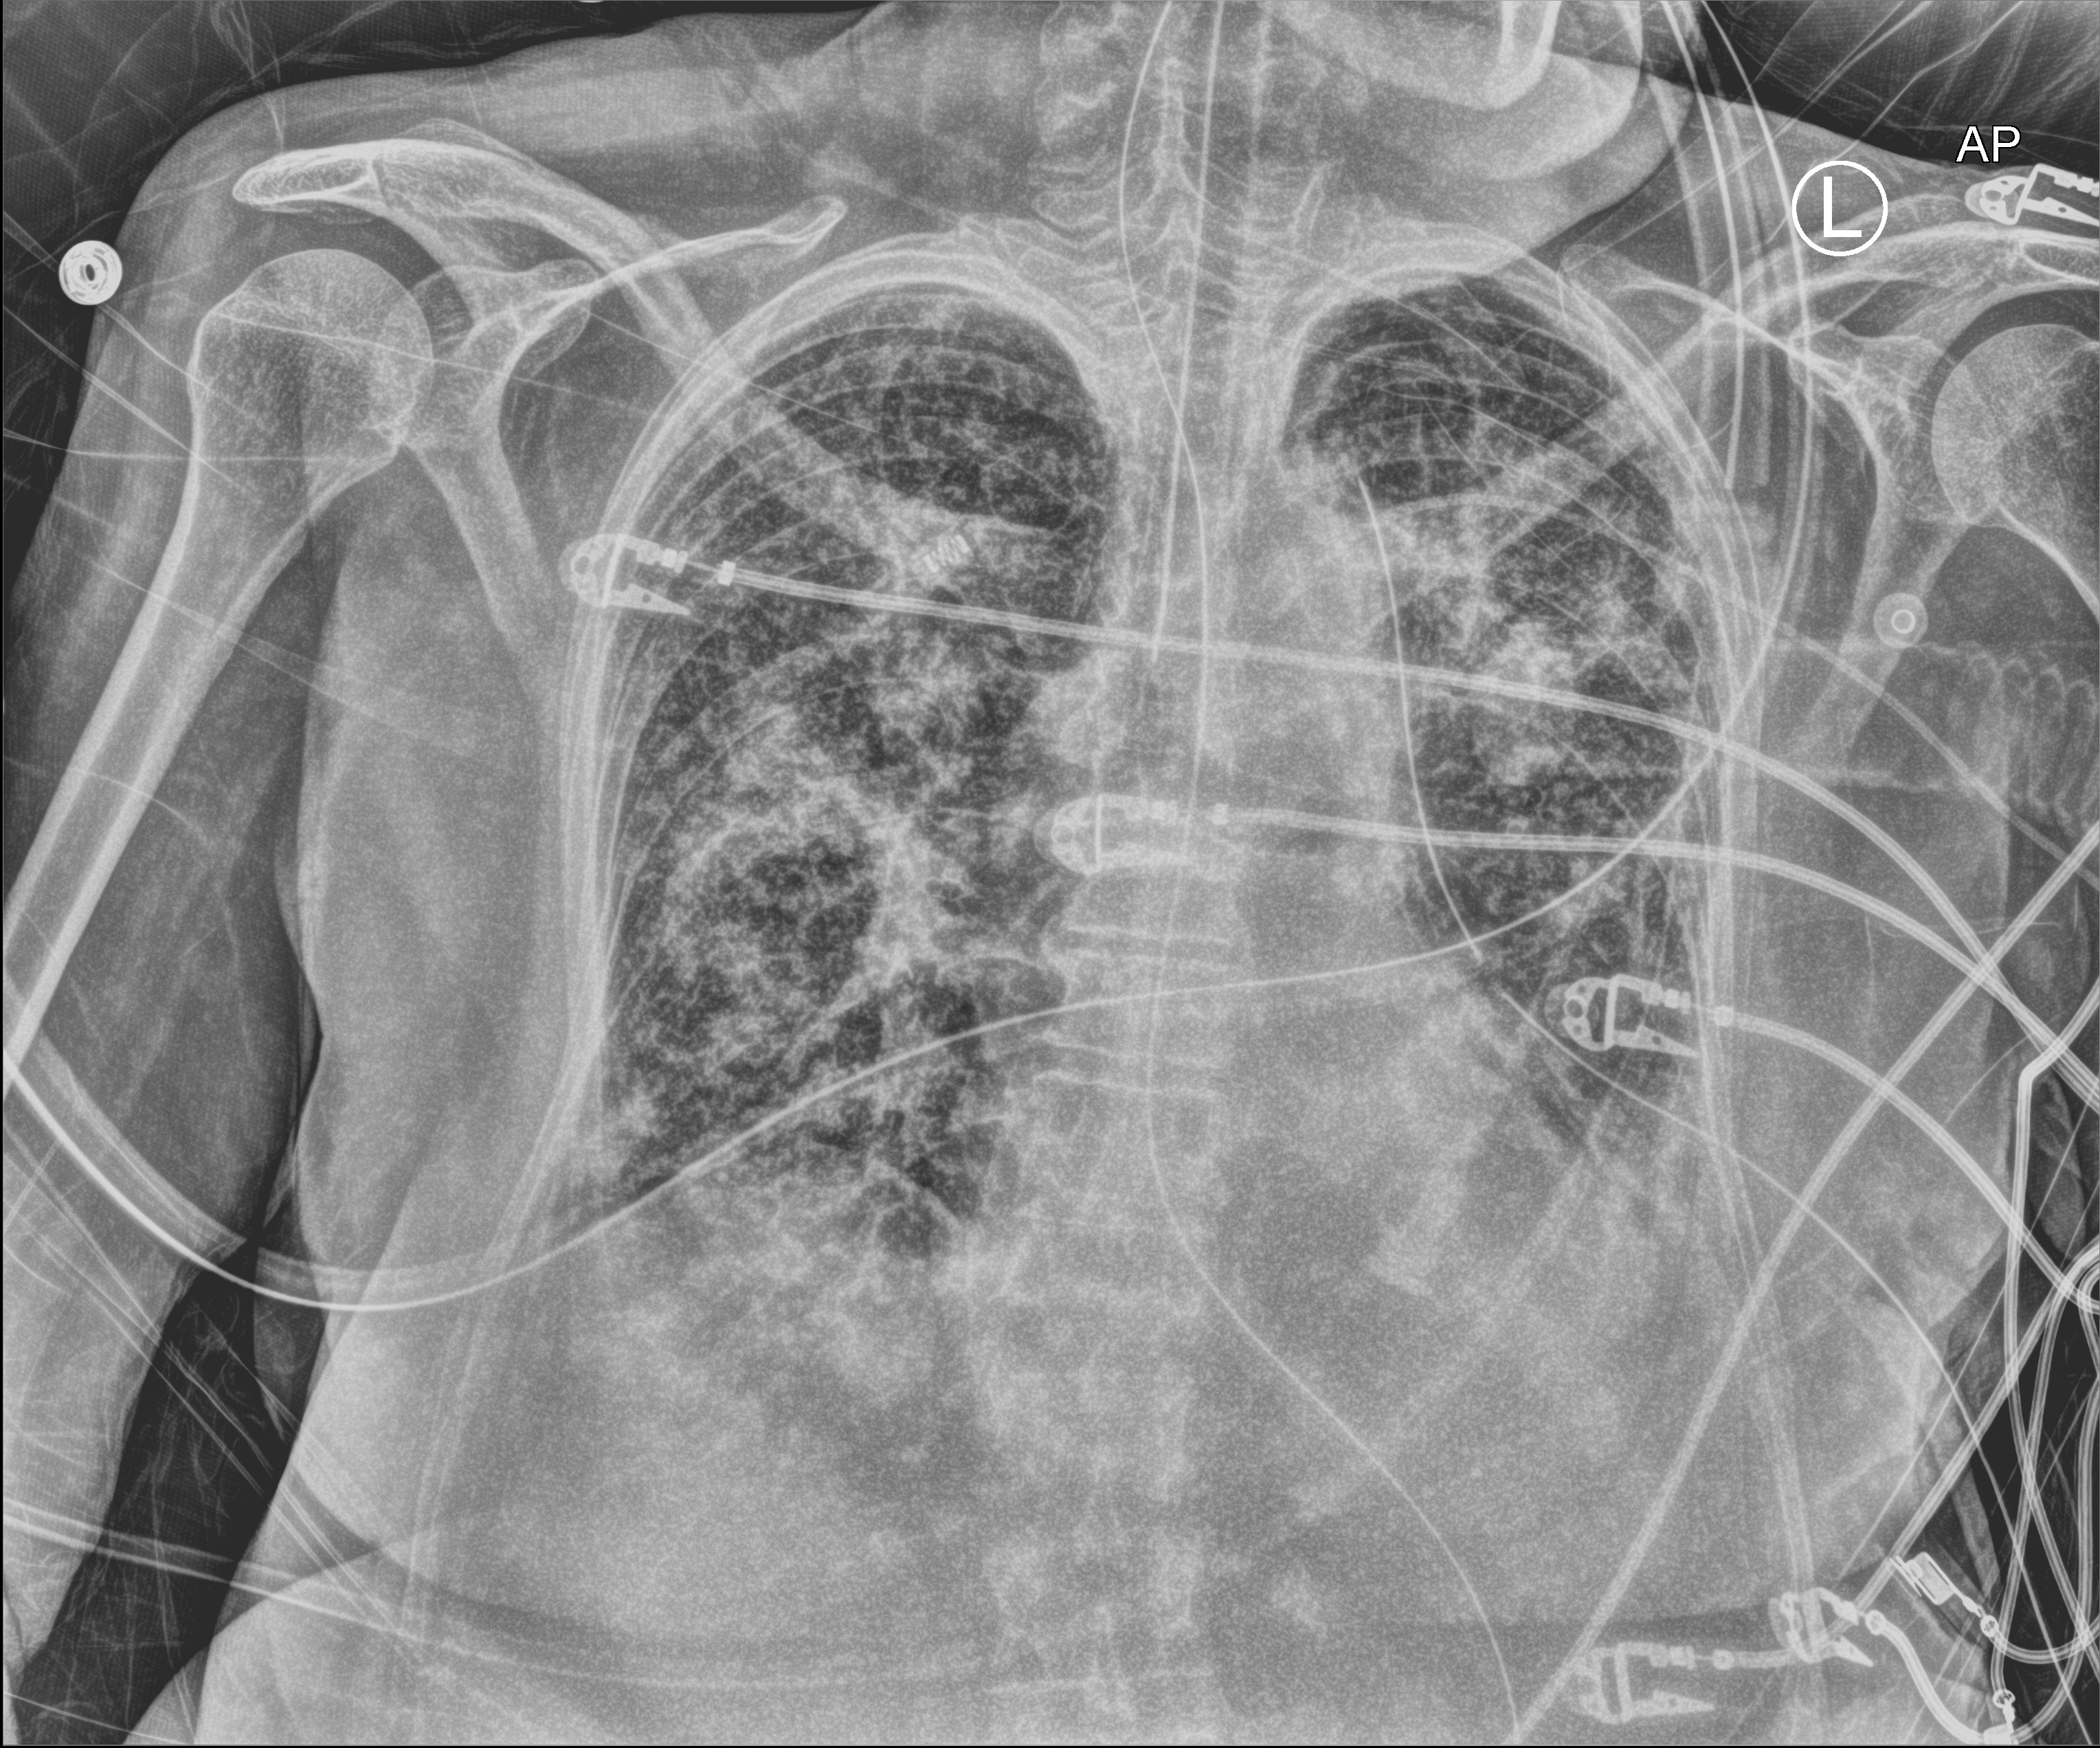
Chest X-ray (portable). Female patient hospitalised with COVID-19, age 75–90 years.
From the hospital-stay record, not from the radiograph (when in the stay this image was taken is not recorded): length of hospital stay: 70 days; mechanically ventilated during this hospital stay: yes; admitted to intensive care during this hospital stay: yes.